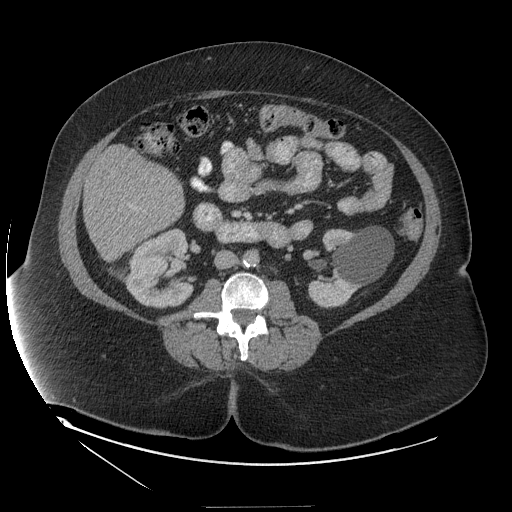
Contrast-enhanced abdominal CT (liver protocol), one axial slice; slice 41 of 127 in the series (ordered by position); reconstruction kernel STANDARD; 140 kVp; soft-tissue window (W 400 / L 40 HU); 2.5 mm slice thickness; 512 × 512 image matrix, field of view 480 × 480 mm. From the clinical record (not read from this slice): diagnosis: hepatocellular carcinoma (patient treated with transarterial chemoembolisation; whether this scan precedes or follows treatment is not stated here); TNM stage (as recorded): Stage-II.
Outlined on this slice (semi-automatic segmentation, software-assisted and operator-edited):
- liver parenchyma outside the tumour (the mass and vessels are separate outlines, so this box may not span the whole liver): bounding box <83,146,184,260> (left, top, right, bottom; pixels)